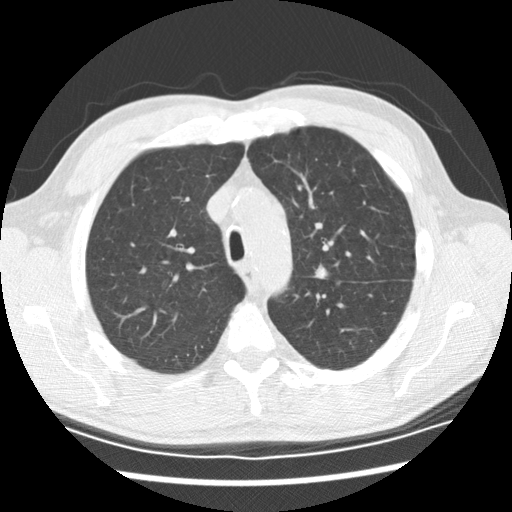
Low-dose screening chest CT, one axial slice; position 152 of 208 along the scan axis; 120 kVp; lung window (W 1500 / L -600 HU); 2.5 mm slice thickness; 512 × 512 image matrix.
Outlined on this slice (outlined manually by an expert reader):
- lesion 1 (tumor, upper lobe of left lung): bounding box (x1, y1, x2, y2) in pixels: (315, 264, 329, 280)